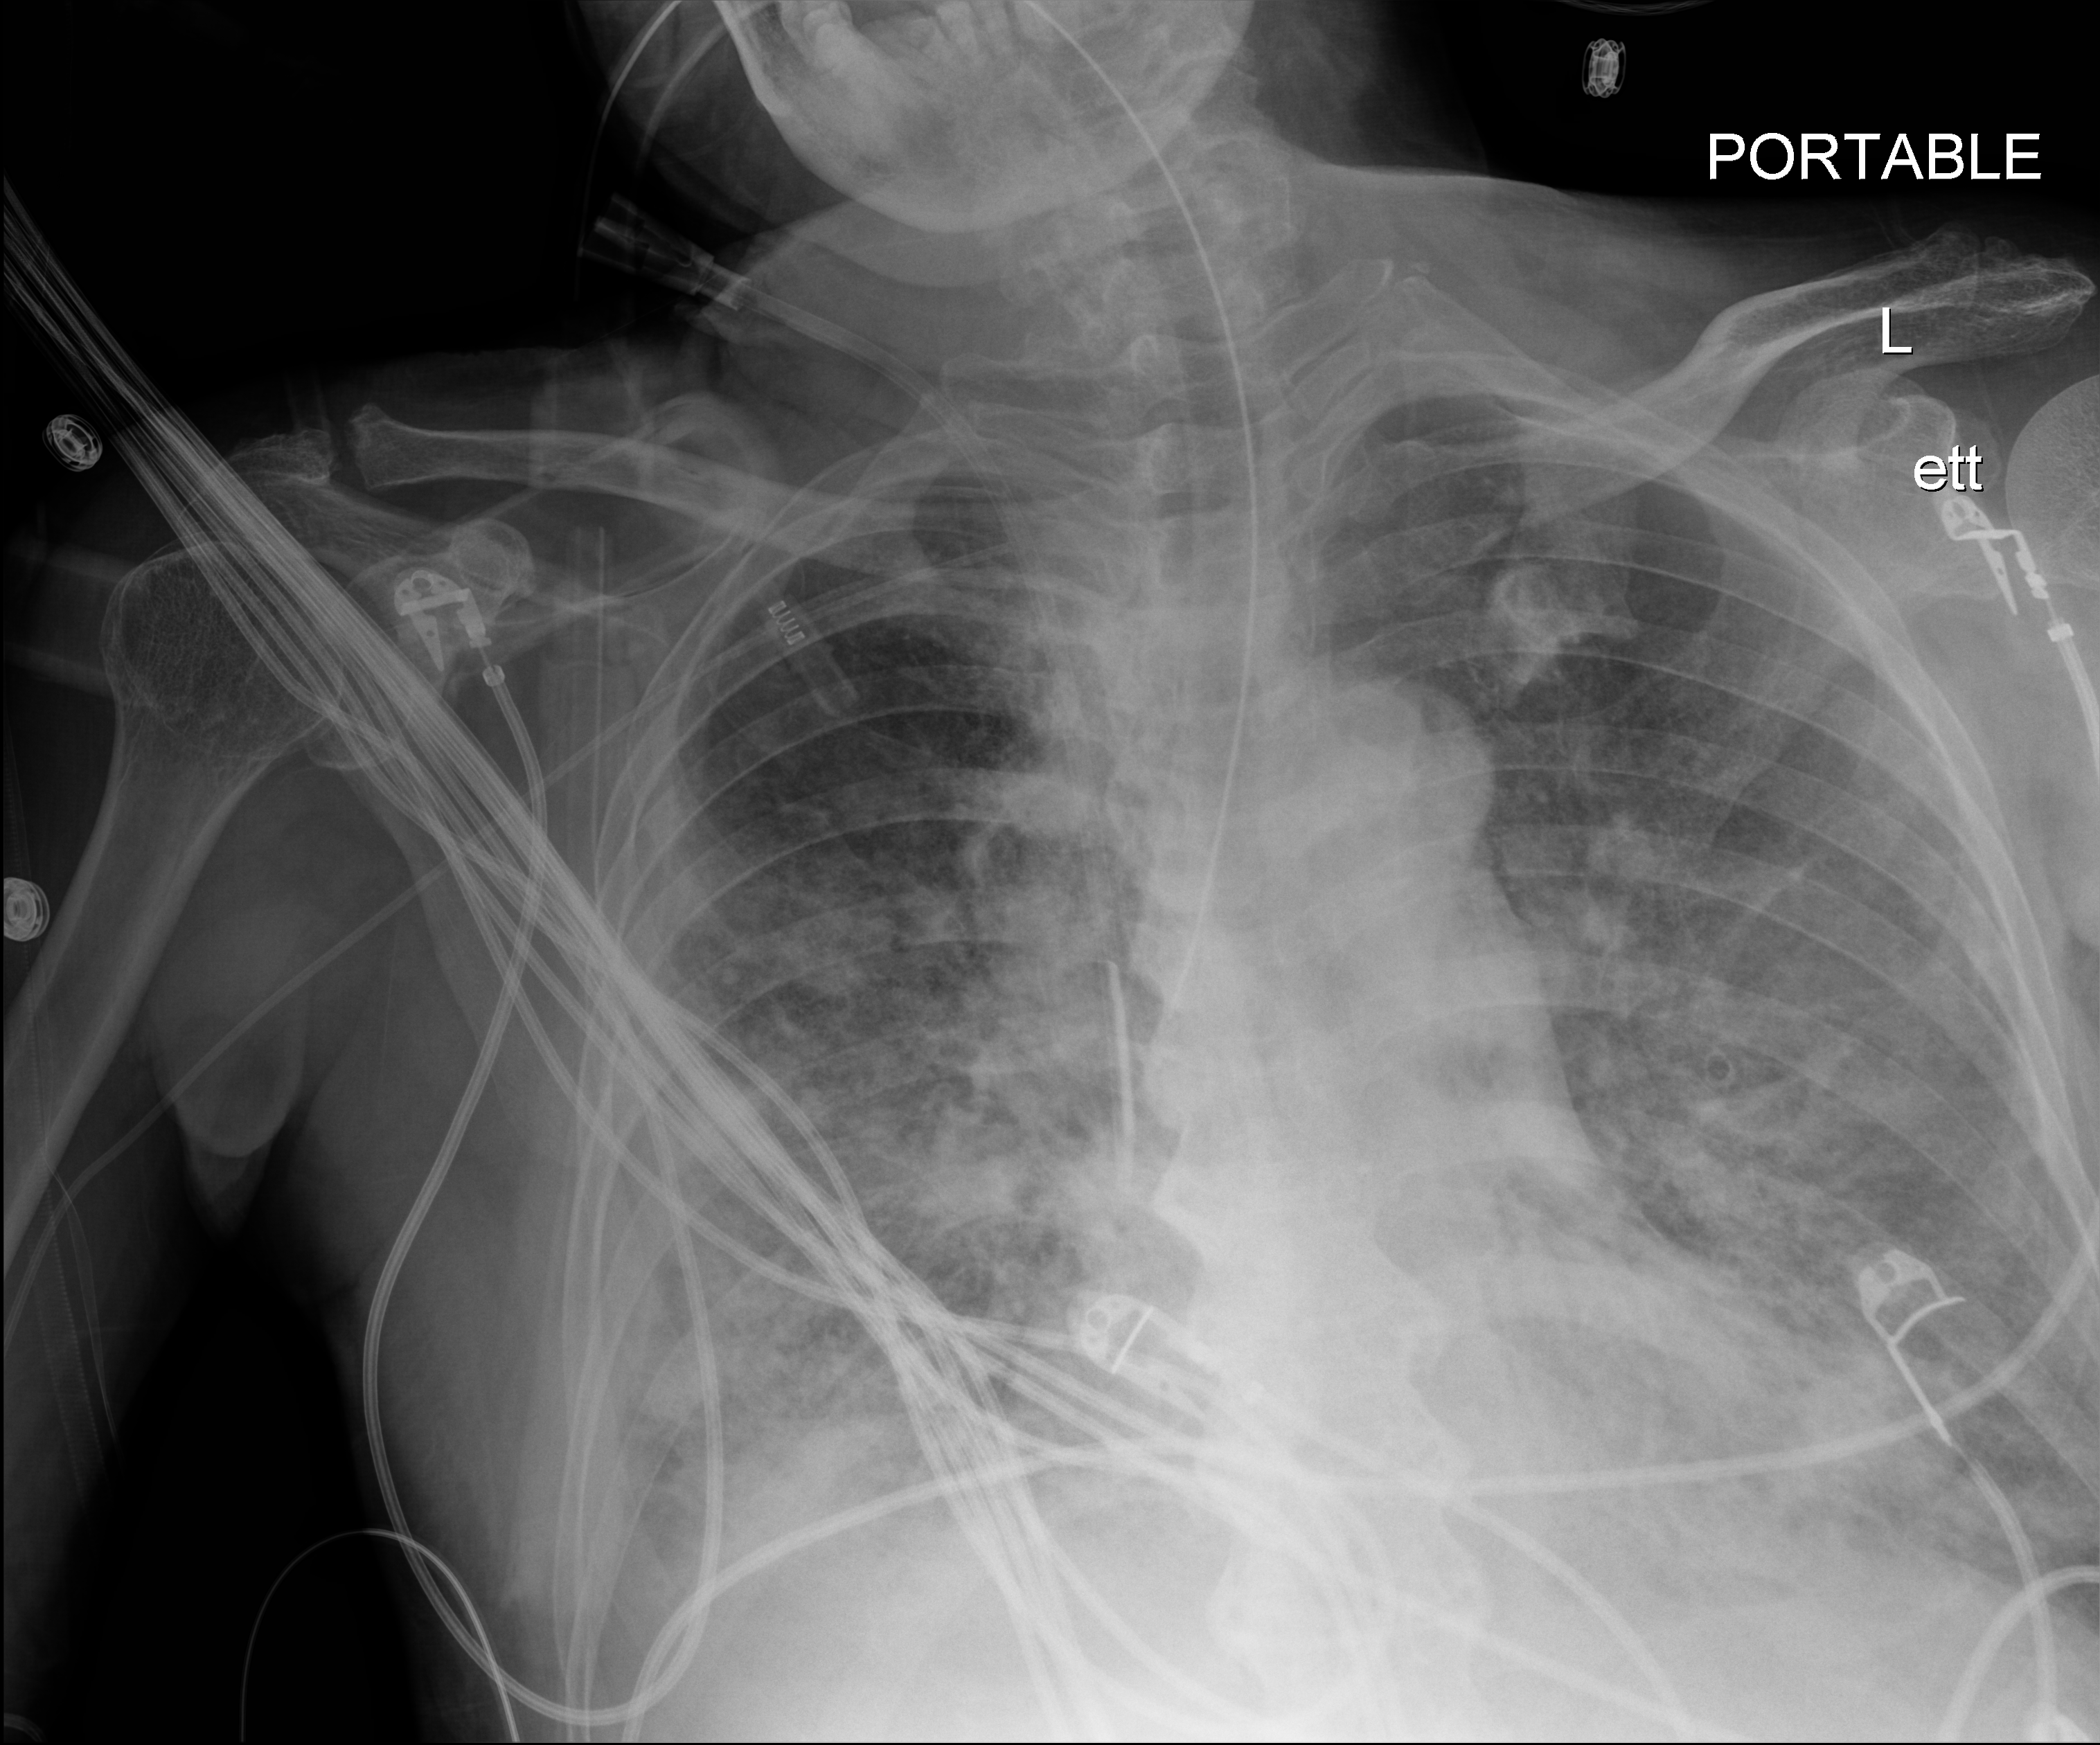
Chest radiograph. Male patient hospitalised with COVID-19, age 60–74 years.
Hospital-stay facts (about this admission, not read from this image; timing relative to this image not recorded): hypertension (admission record): yes; chronic kidney disease (admission record): no.